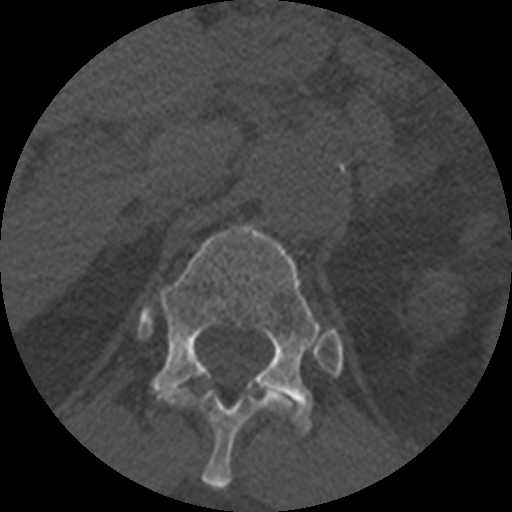
CT including the spine, one axial slice. Position 394 of 399 along the scan axis. 120 kVp. Bone window (W 1800 / L 400 HU). 1.25 mm slice thickness. 512 × 512 image matrix, field of view 160 × 160 mm. Patient age 71 years. Case-level facts recorded for this patient, not image findings: primary cancer: prostate.
Annotated regions visible in this slice (semi-automatic segmentation, software-assisted and operator-edited):
- T11 vertebra: bounding box (x1, y1, x2, y2) in pixels: (160, 390, 299, 490)
- T12 vertebra: (150, 224, 322, 435)